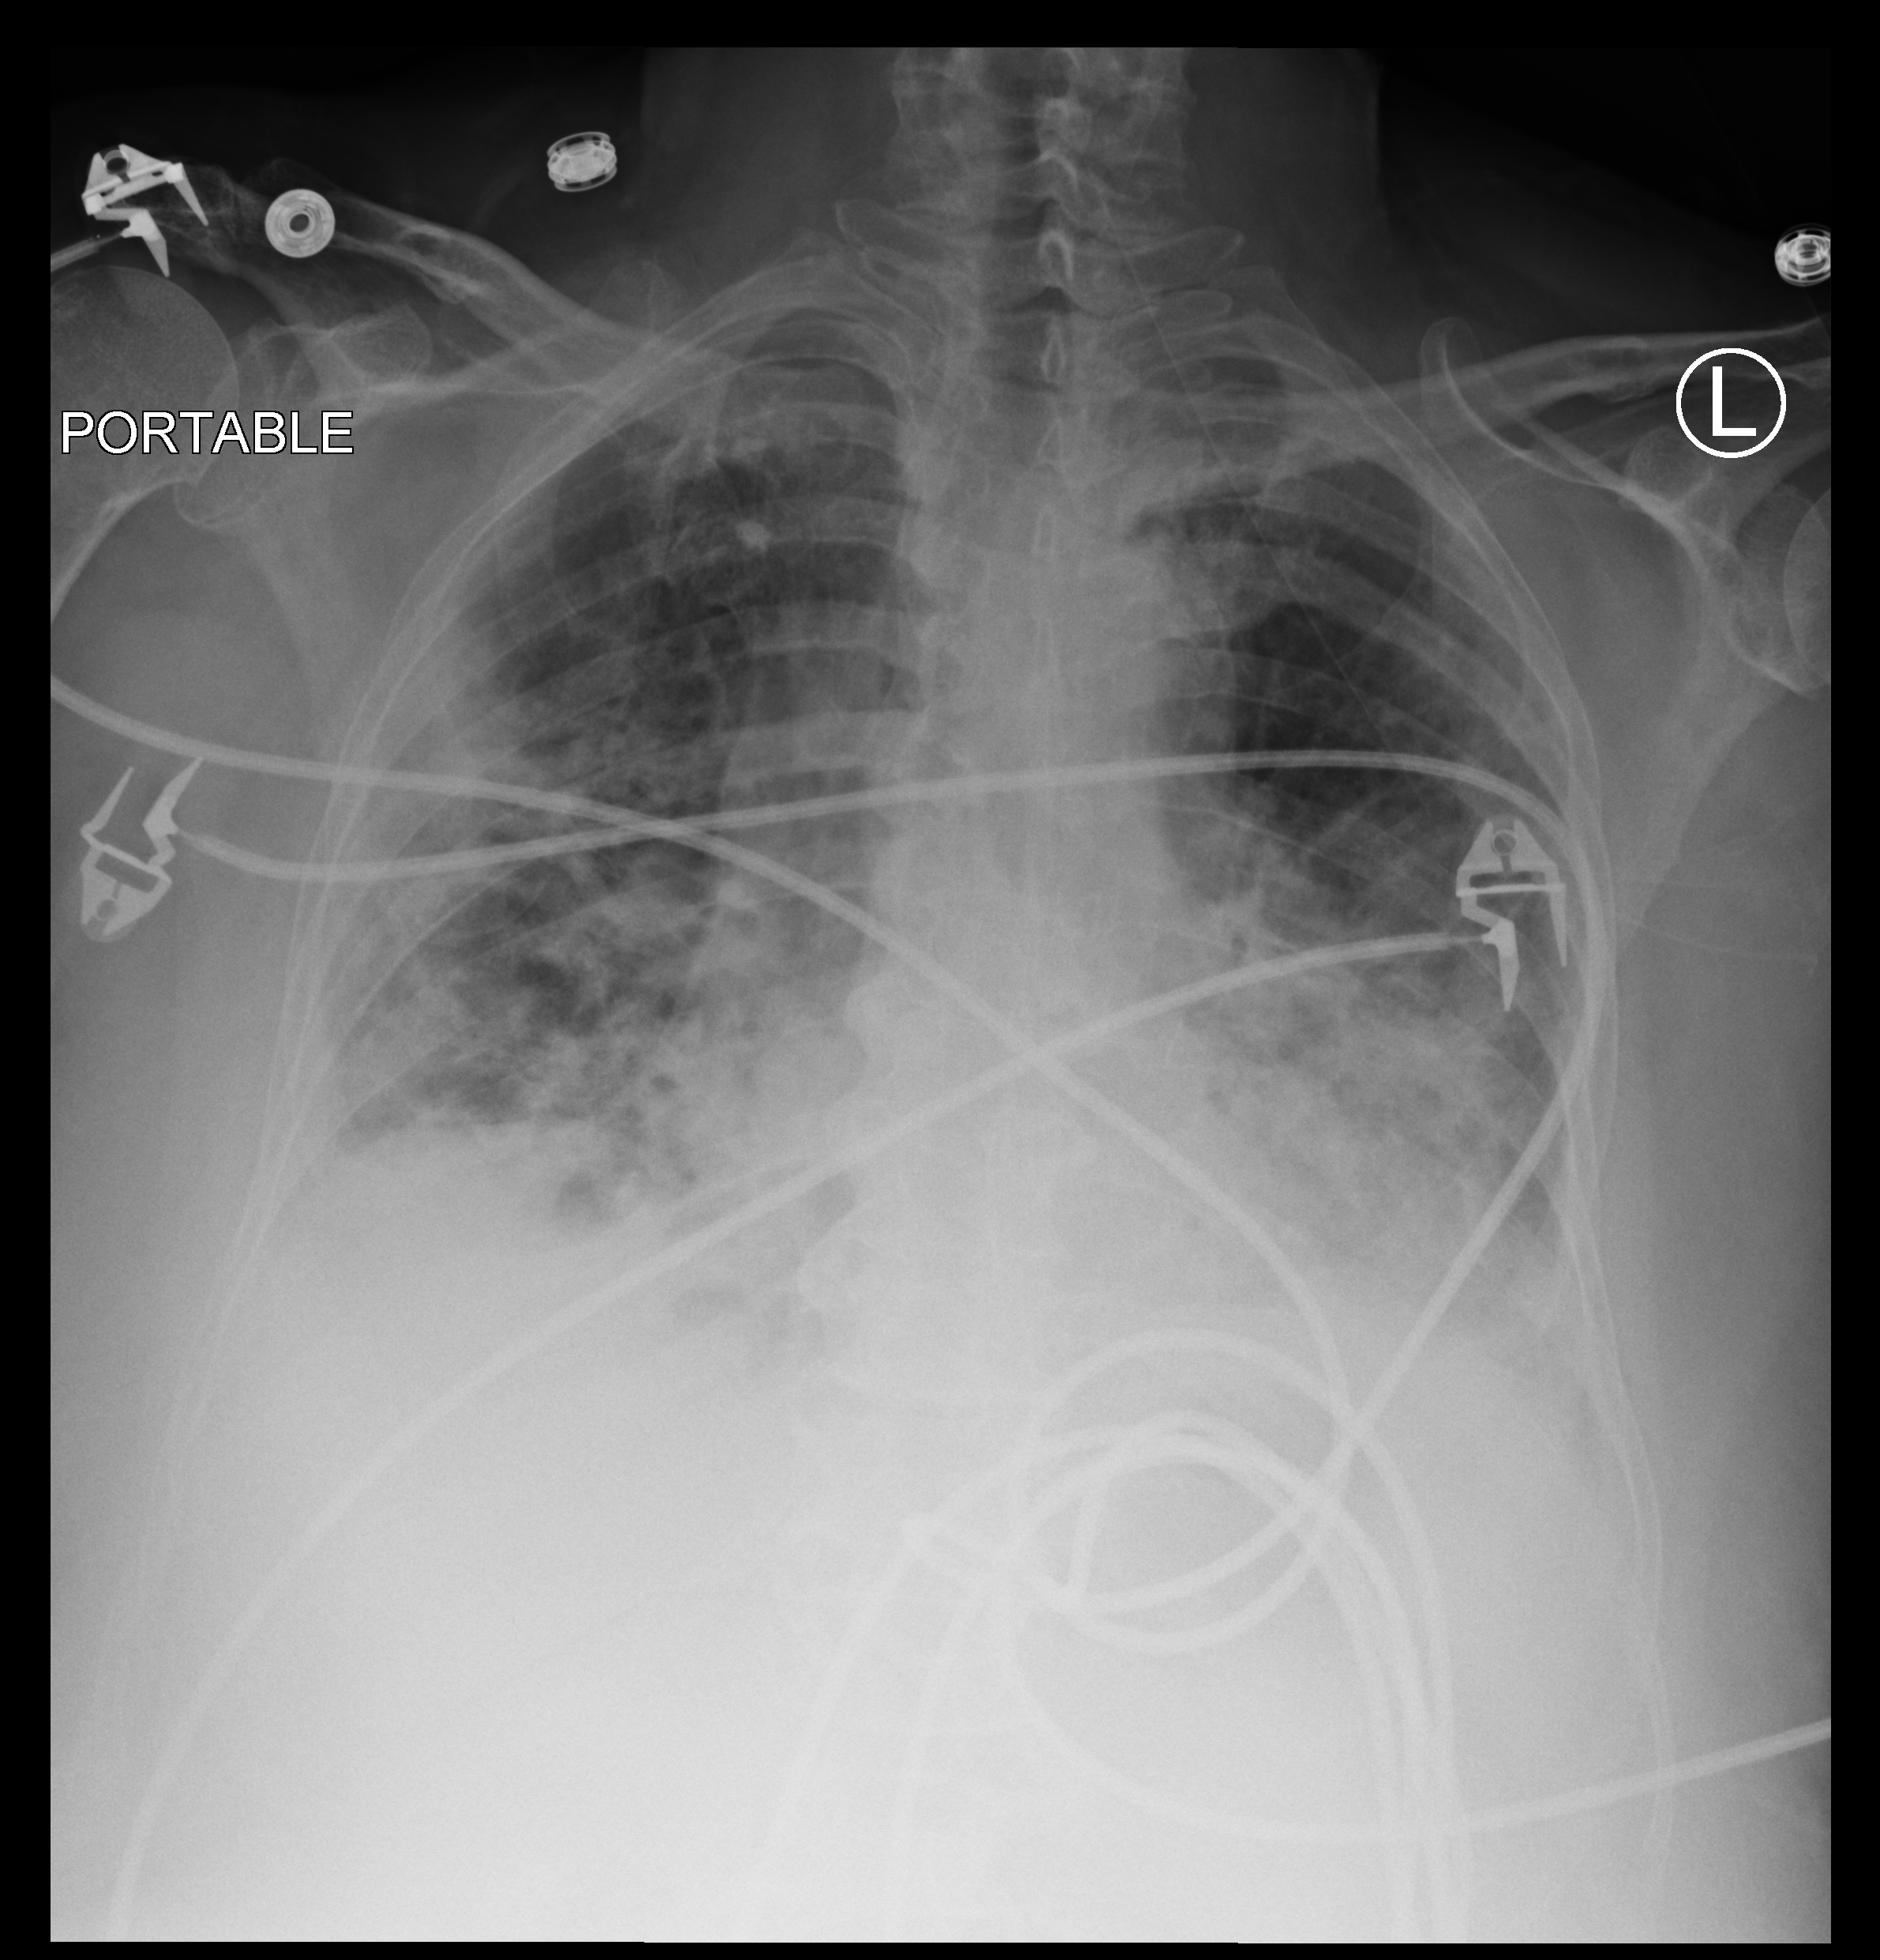
Portable chest radiograph. Patient hospitalised with COVID-19; female, aged 75–90 years.
From the hospital-stay record, not from the radiograph (when in the stay this image was taken is not recorded):
- COPD (admission record): yes
- admitted to intensive care during this hospital stay: yes
- mechanically ventilated during this hospital stay: no